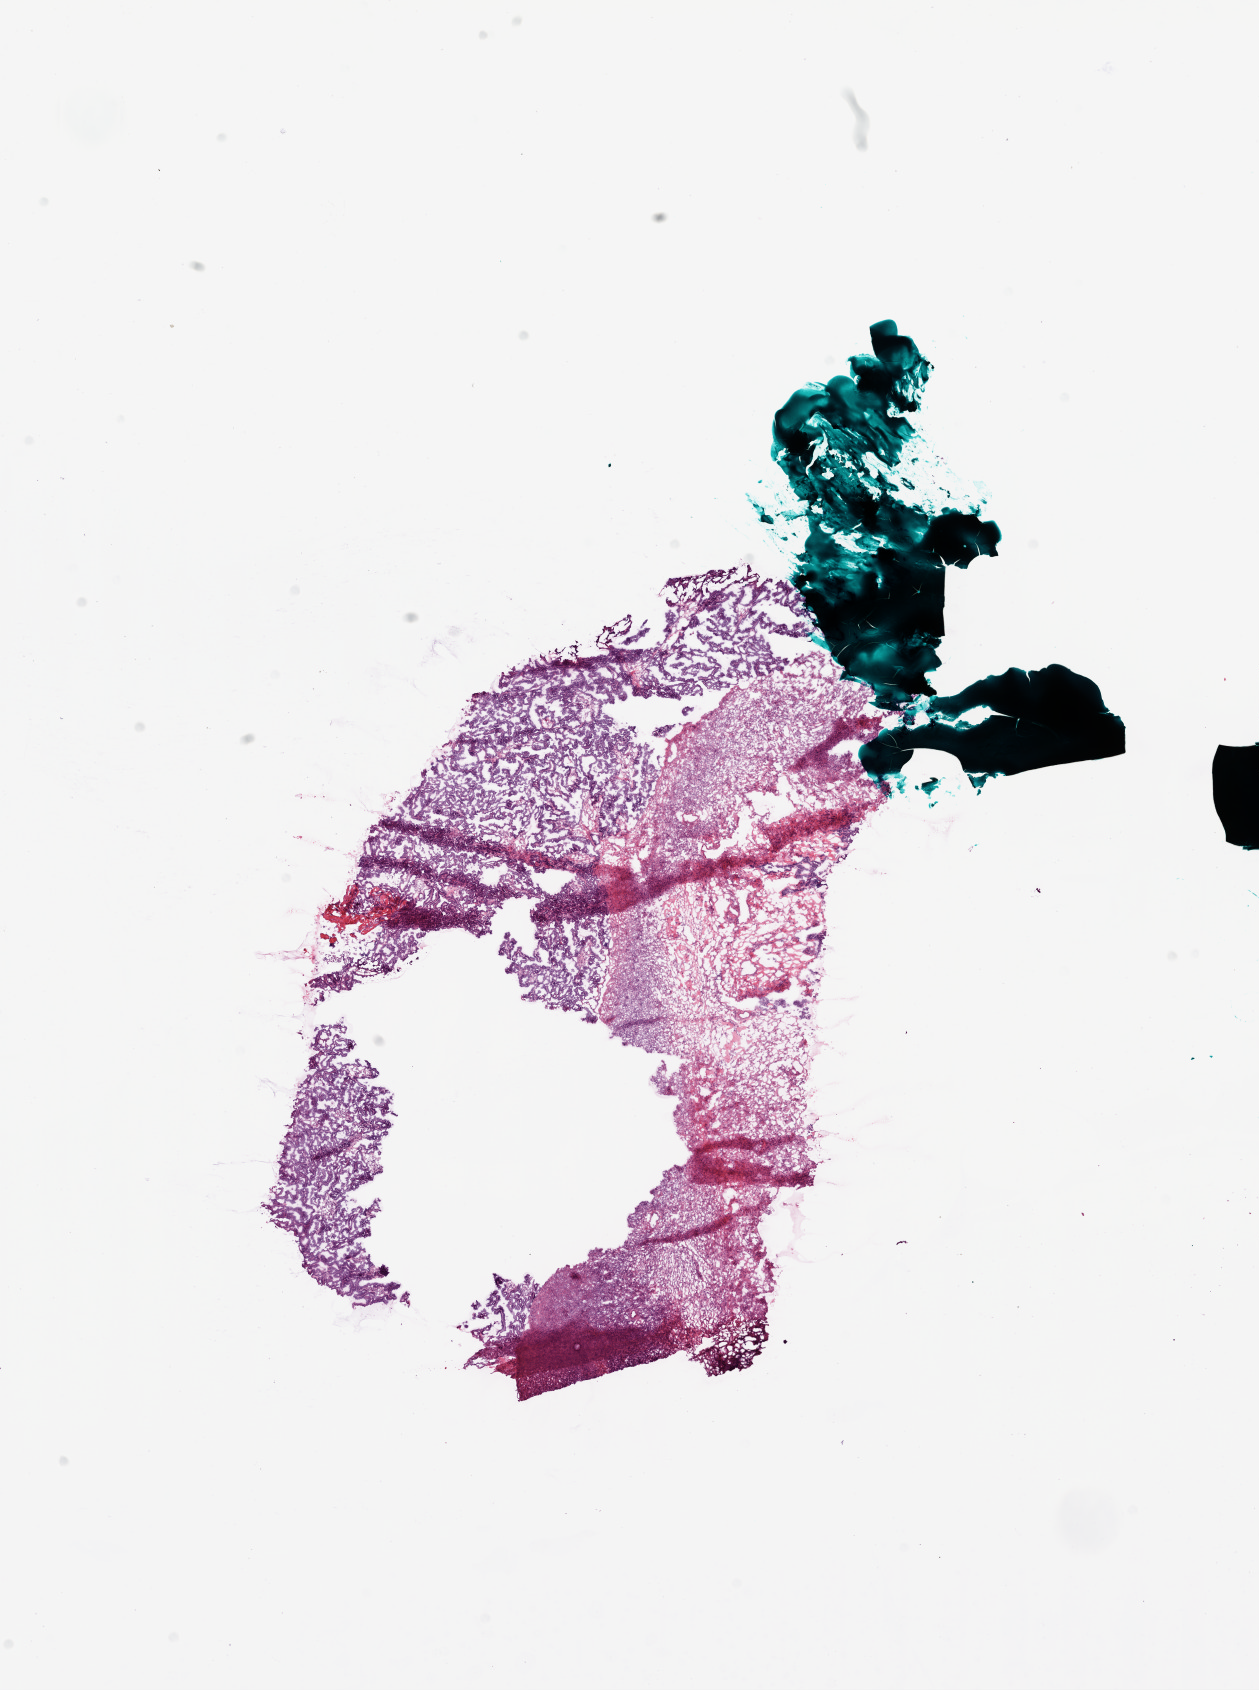
Whole-slide histology image, H&E-stained, shown as a low-resolution overview of the whole scanned area (about 10.2 x 13.6 mm), frozen section from the bottom of the tissue portion, ovary, primary tumour sample. Patient: female, age at initial diagnosis 65 years. Histologic grade: G2 (moderately differentiated). Slide review estimates, as recorded: tumour cells 60%, tumour nuclei 75%, normal cells 10%, stromal cells 30%, necrosis 0%.
Histologic diagnosis: Serous cystadenocarcinoma, NOS. FIGO stage: IIIC.